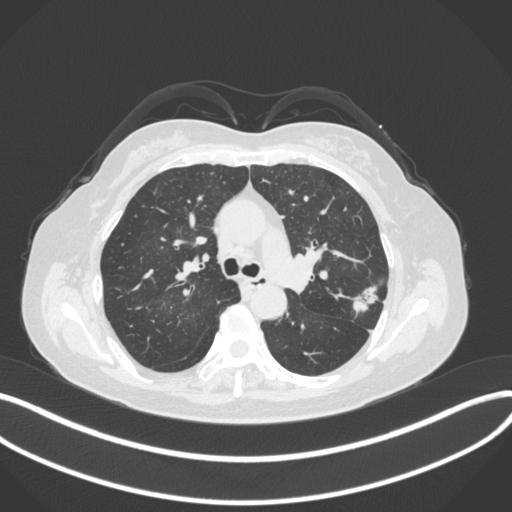
Chest CT, one axial slice. Position 219 of 330 along the scan axis. Reconstruction kernel B31f. 120 kVp. Lung window (W 1500 / L -600 HU). 512 × 512 image matrix. Female patient, age 60 years. Case-level facts recorded for this patient, not image findings: clinical TNM (as recorded): T1c N0 M0.
Annotated regions visible in this slice (rectangle marked by the reading radiologist):
- lung tumour (recorded histology: adenocarcinoma): bounding box (x1, y1, x2, y2) in pixels: (349, 279, 383, 316)